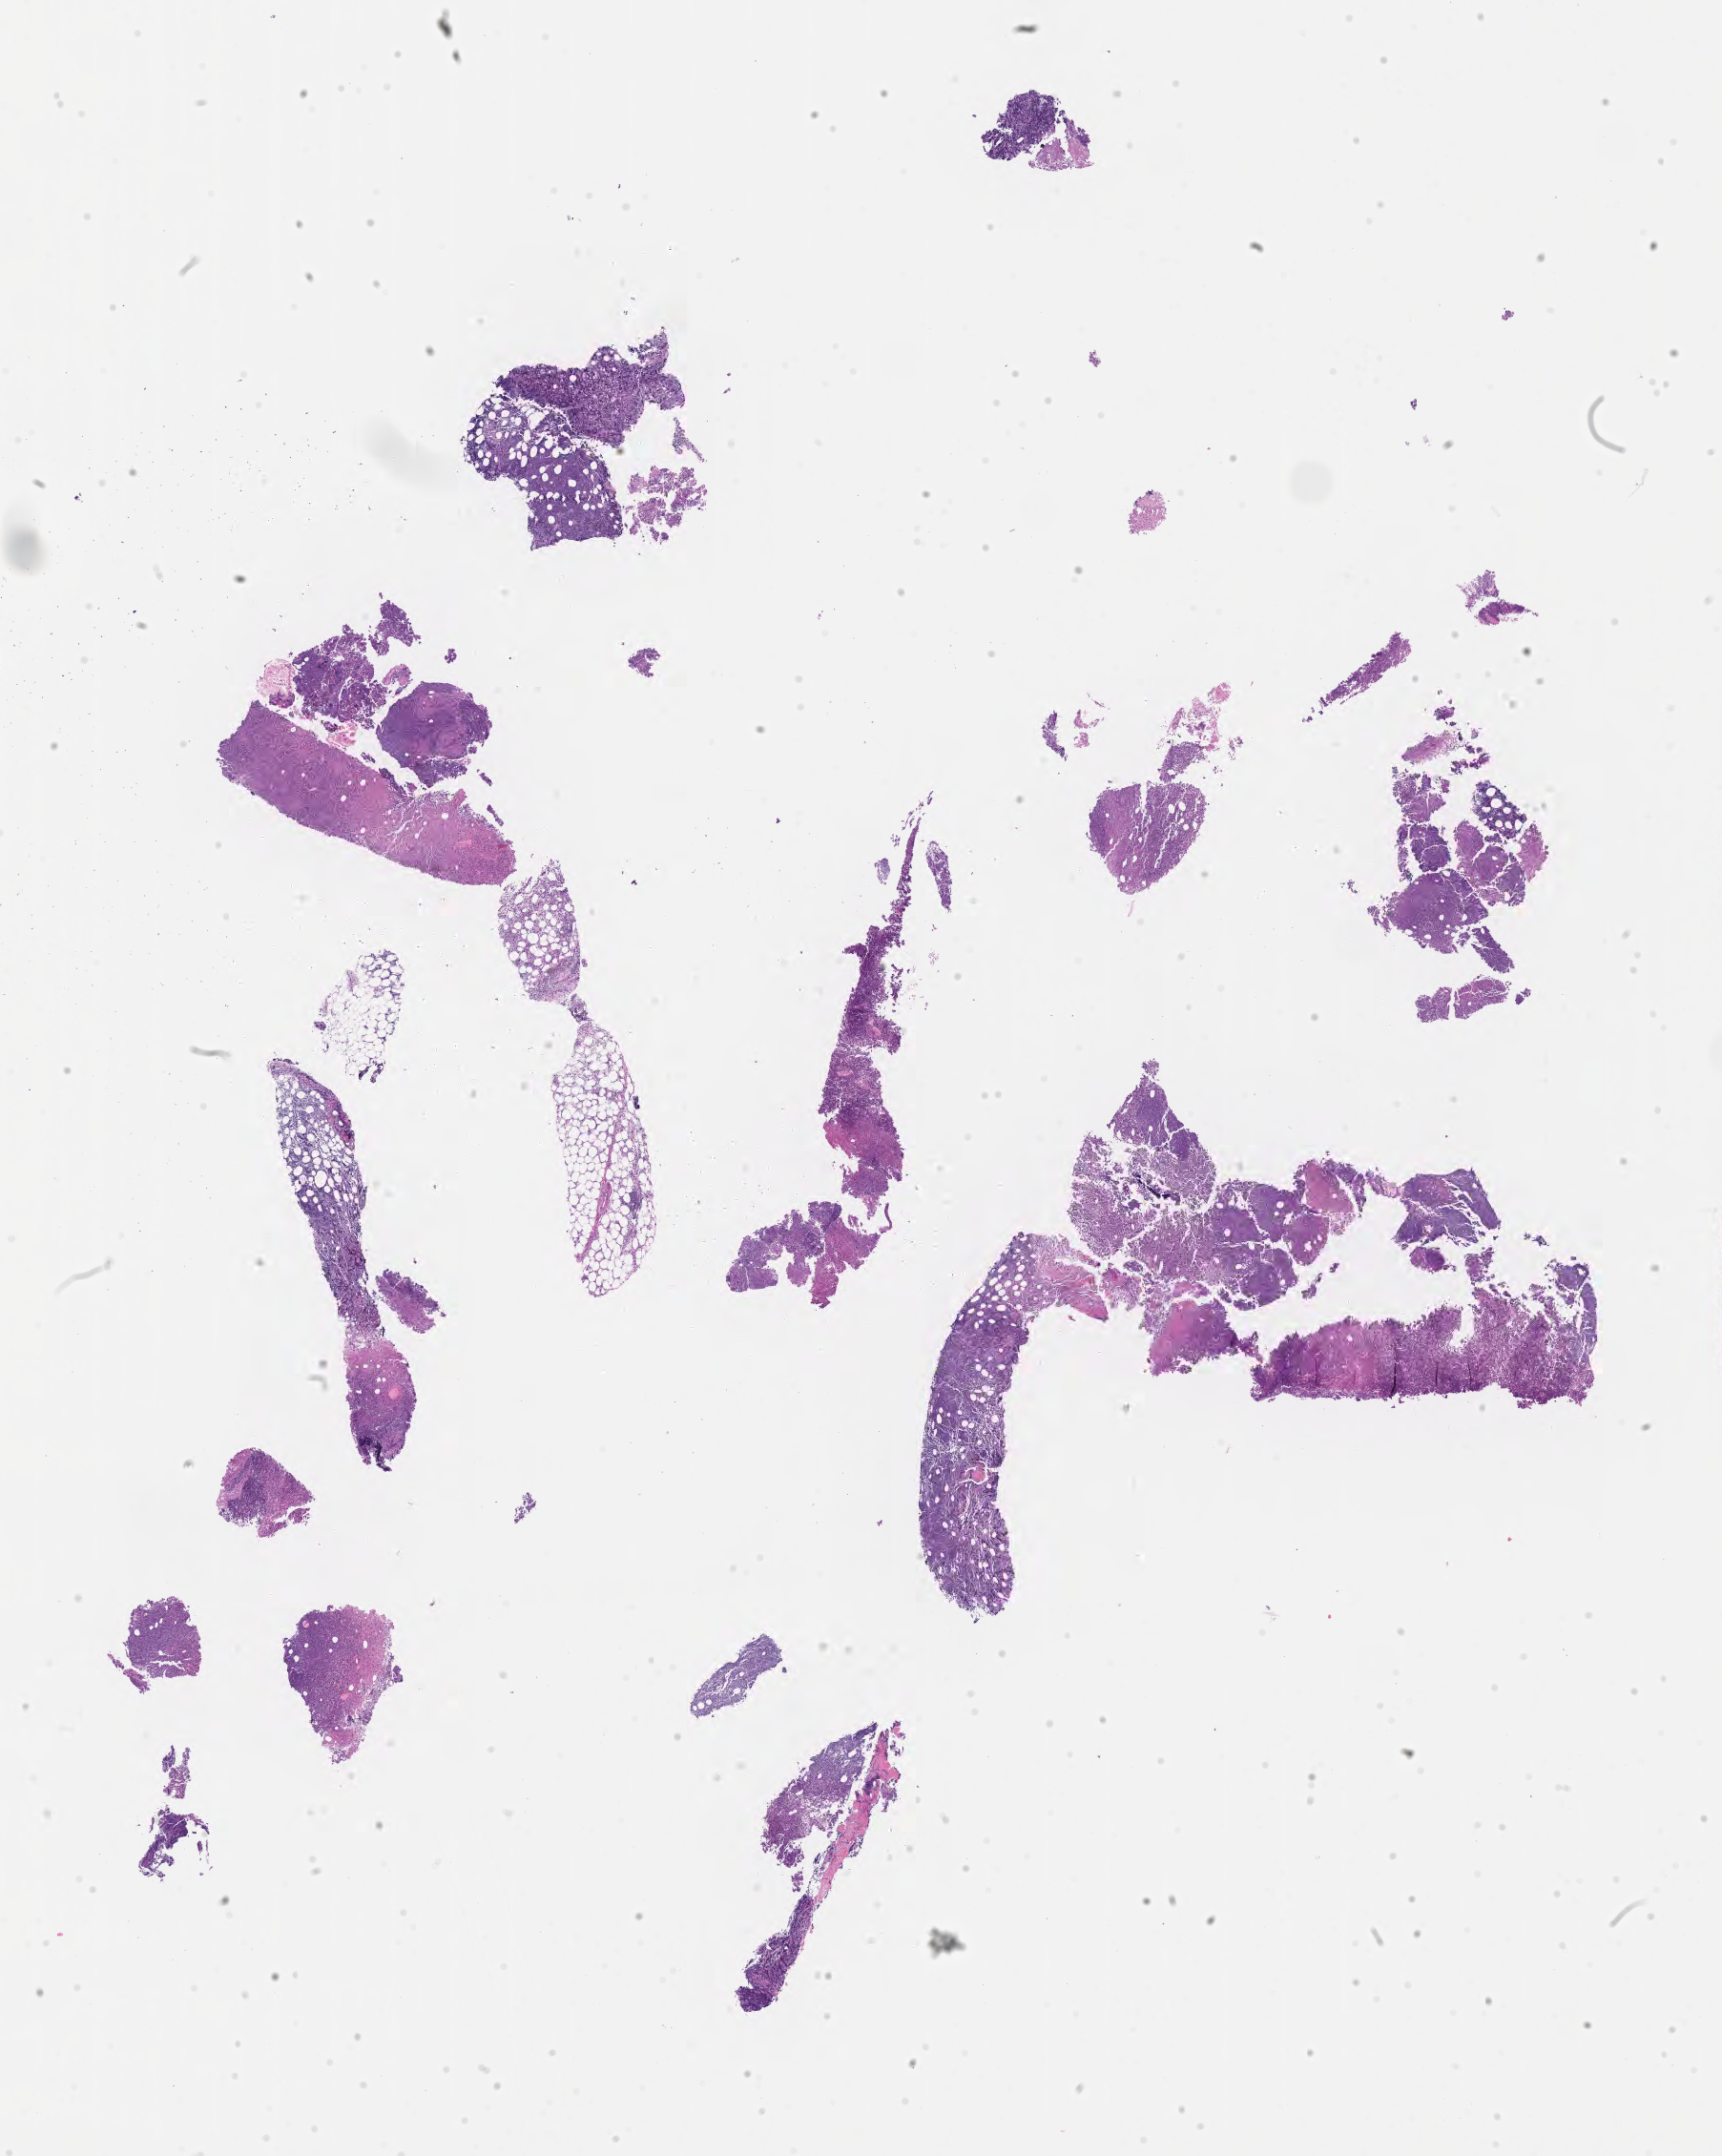
Digitized hematoxylin and eosin (H&E)-stained section, low-resolution overview of the scanned area, about 14.6 x 18.3 mm. Tumor tissue. Anatomic site: pelvis. Patient: female, aged 64.
Histologic diagnosis: Burkitt lymphoma, NOS.